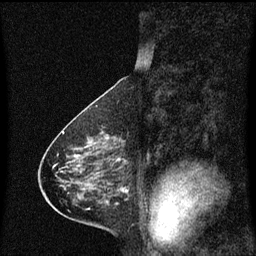
Breast MRI (dynamic contrast-enhanced), one sagittal slice. Position 31 of 60 along the scan axis. Dynamic contrast-enhanced series, image 2 of 3 at this slice position (ordered by acquisition). 1.5 T. TE 4.2 ms, TR 8.4 ms. 256 × 256 image matrix, field of view 200 × 200 mm. Patient: female, 58 years.
Annotated regions visible in this slice (semi-automatically segmented with operator editing):
- analysis volume of interest (the breast-tissue region the enhancement analysis was run in; not a lesion): box from (x=100, y=131) to (x=125, y=160) px
- tumour enhancement mask (voxels above the 70 % enhancement threshold inside the analysis volume of interest): (x=118, y=158)–(x=121, y=160)